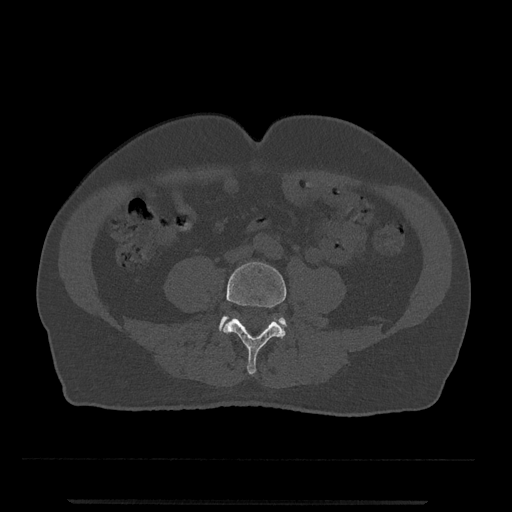
CT including the spine, one axial slice. Position 122 of 797 along the scan axis. 120 kVp. Bone window (W 1800 / L 400 HU). 0.5 mm slice thickness. 512 × 512 image matrix, field of view 419 × 419 mm. Male patient, age 63 years. Case-level facts recorded for this patient, not image findings: primary cancer: prostate.
Structures marked on this image (semi-automatically segmented with operator editing):
- L4 vertebra: box from (x=223, y=262) to (x=286, y=375) px
- L5 vertebra: (x=219, y=316)–(x=286, y=331)